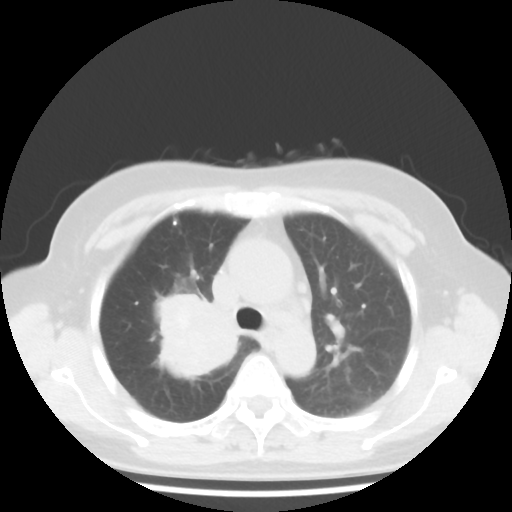
Chest CT, one axial slice; position 29 of 43 along the scan axis; reconstruction kernel STANDARD; lung window (W 1500 / L -600 HU); 5 mm slice thickness; 512 × 512 image matrix, field of view 316 × 316 mm. Female patient, age 62 years. Case-level facts recorded for this patient, not image findings: clinical TNM (as recorded): T3 N0 M0.
Annotated regions visible in this slice (bounding box drawn by a radiologist):
- lung tumour (recorded histology: small cell carcinoma): bounding box <145,290,245,385> (left, top, right, bottom; pixels)